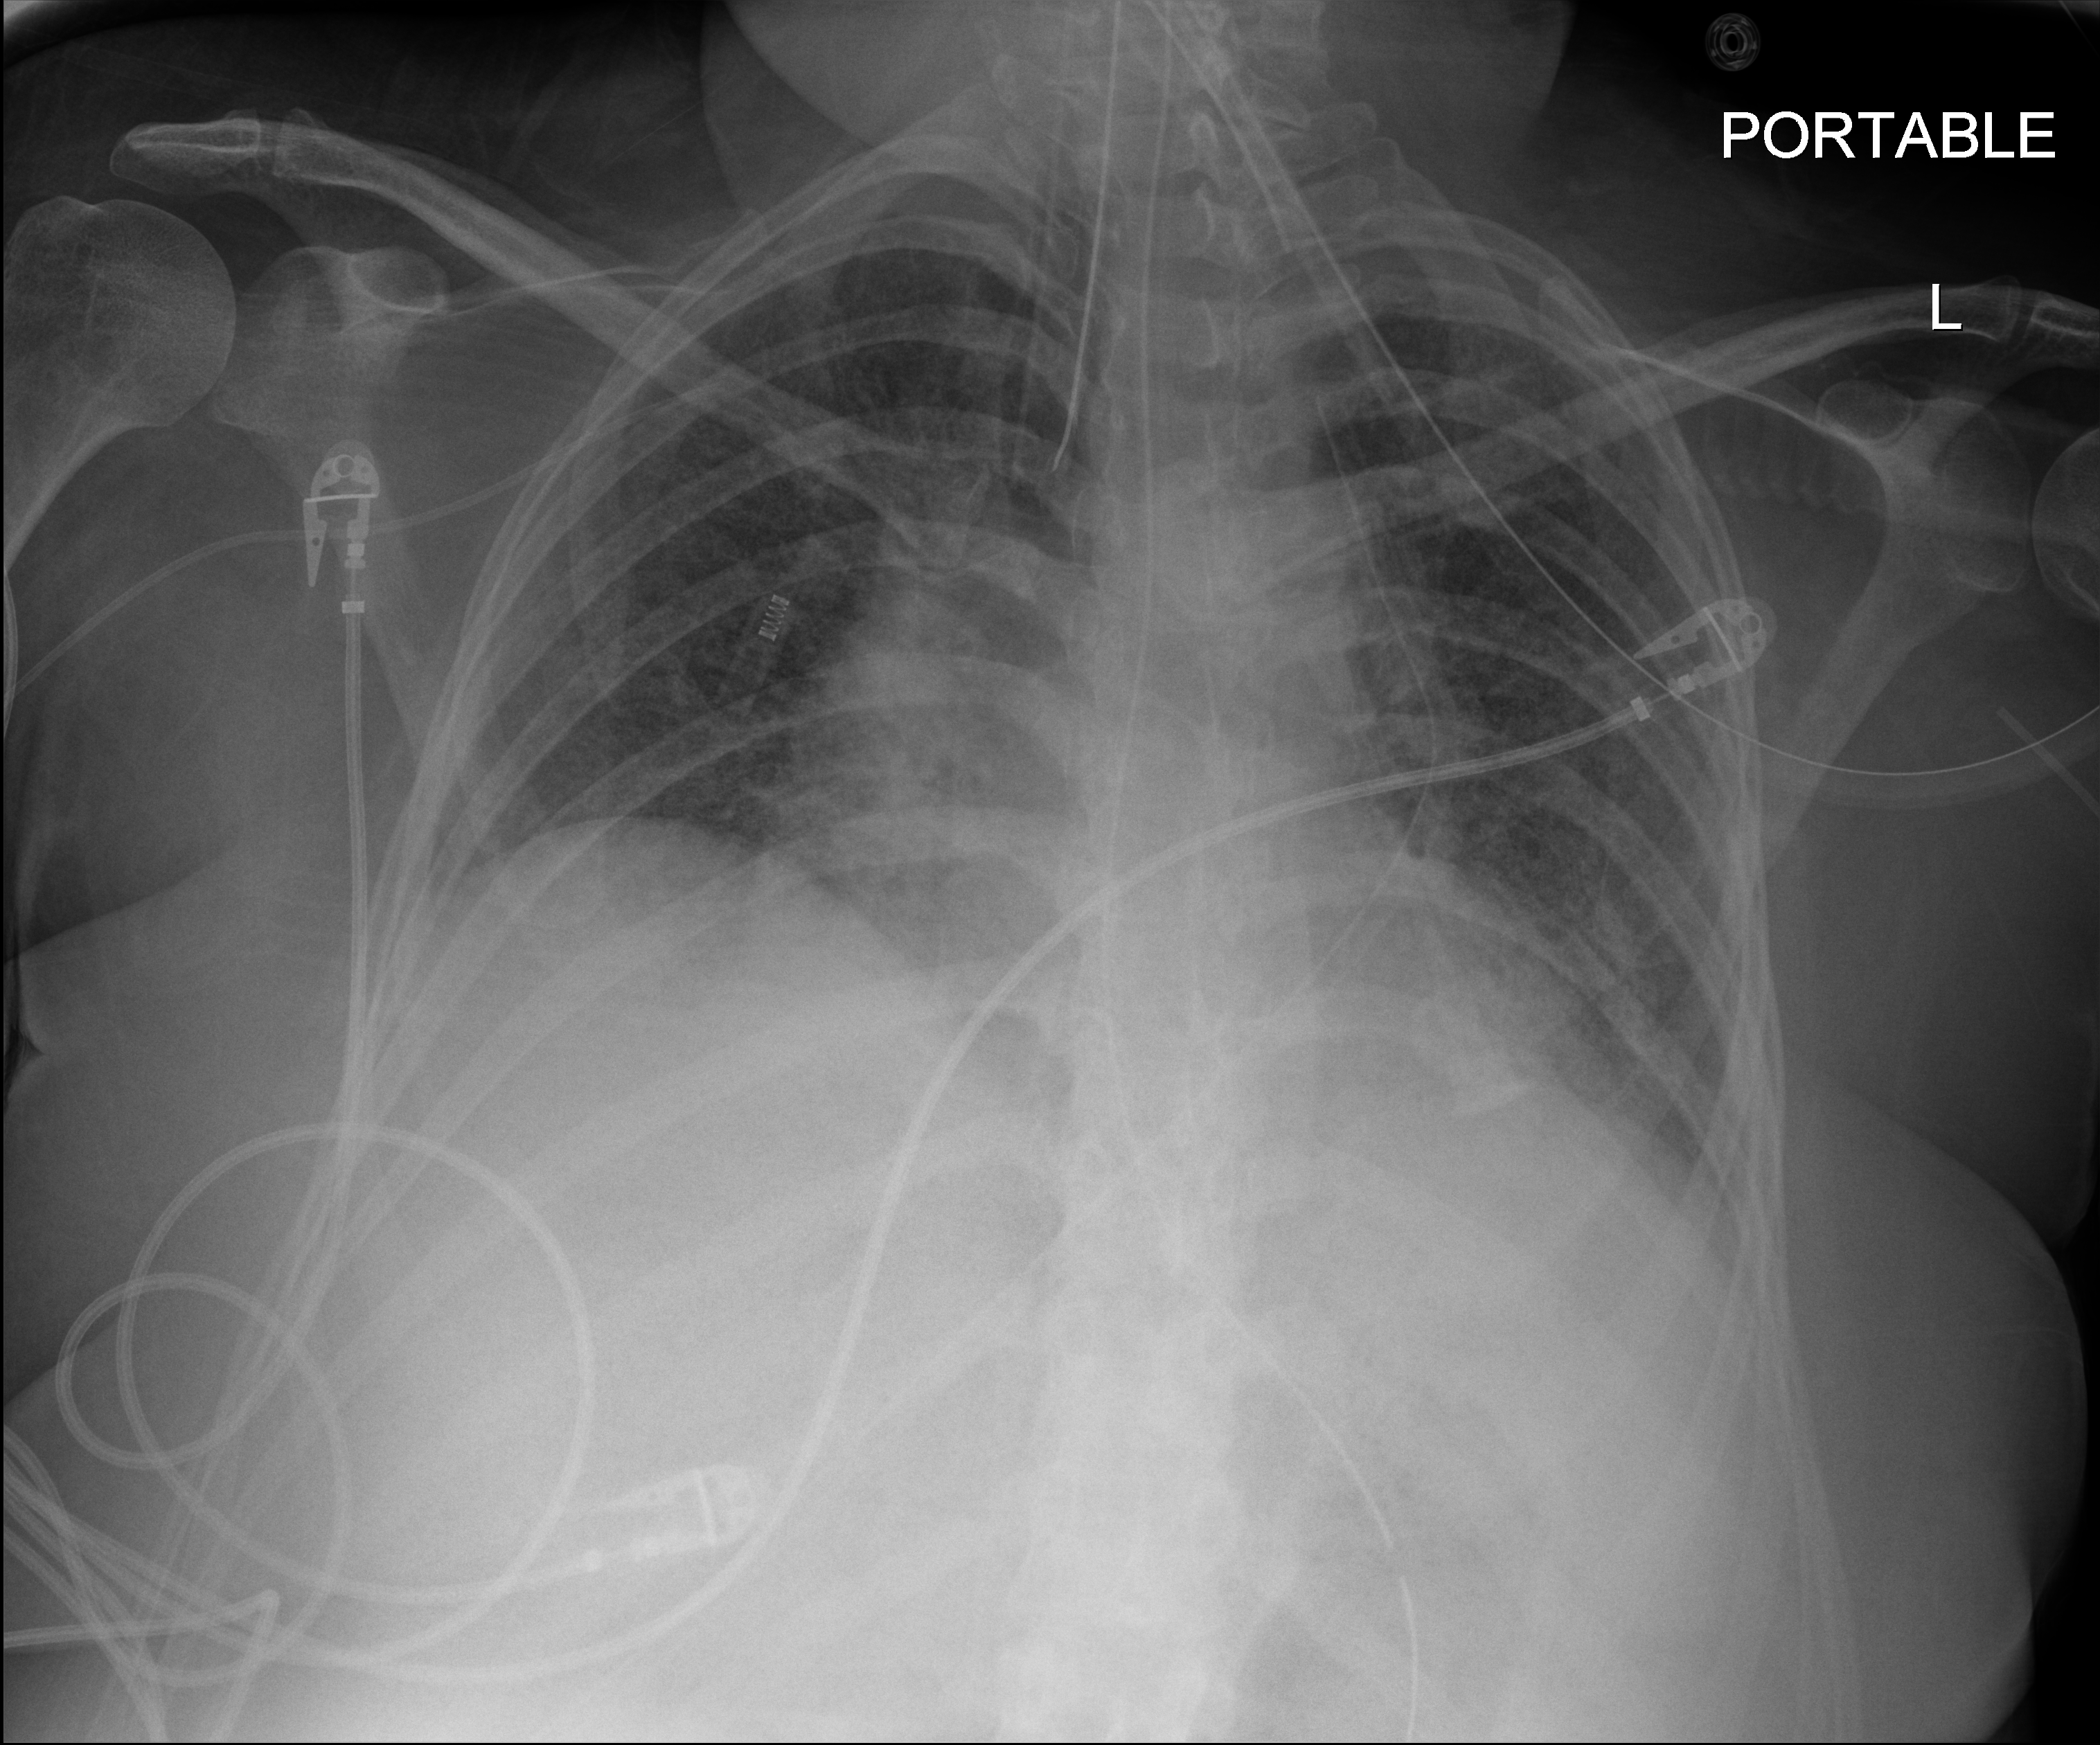
Bedside chest radiograph (digital radiography). Patient hospitalised with COVID-19; female, aged 18–59 years.
From the hospital-stay record, not from the radiograph (when in the stay this image was taken is not recorded):
- admitted to intensive care during this hospital stay: yes
- length of hospital stay: 73 days